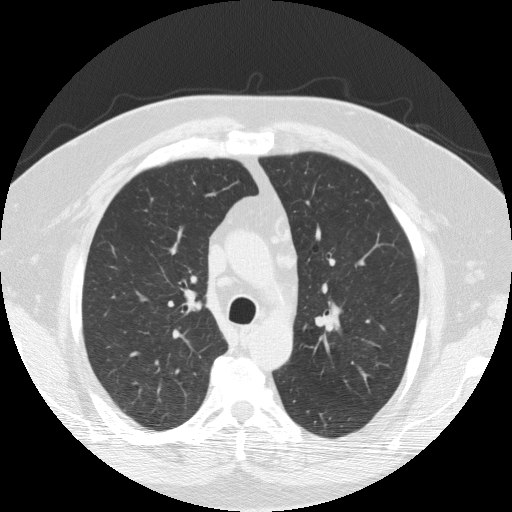
Low-dose screening chest CT, axial slice; second annual screen; lung window (W 1500 / L -600 HU); 2 mm slice thickness; 512 × 512 image matrix. Male participant, aged 60 years at enrolment. Current smoker at enrolment.
- Expert reader's lesion annotation, bounding box <315,306,343,337> (left, top, right, bottom; pixels).
- No non-calcified nodule or mass ≥4 mm was recorded by the screening reader at this exam.
- Official screen result: negative screen, significant abnormalities not suspicious for lung cancer.
- Later outcome: lung cancer diagnosed 425 days after this screen — squamous cell carcinoma, NOS, right upper lobe, 27 mm at pathology.